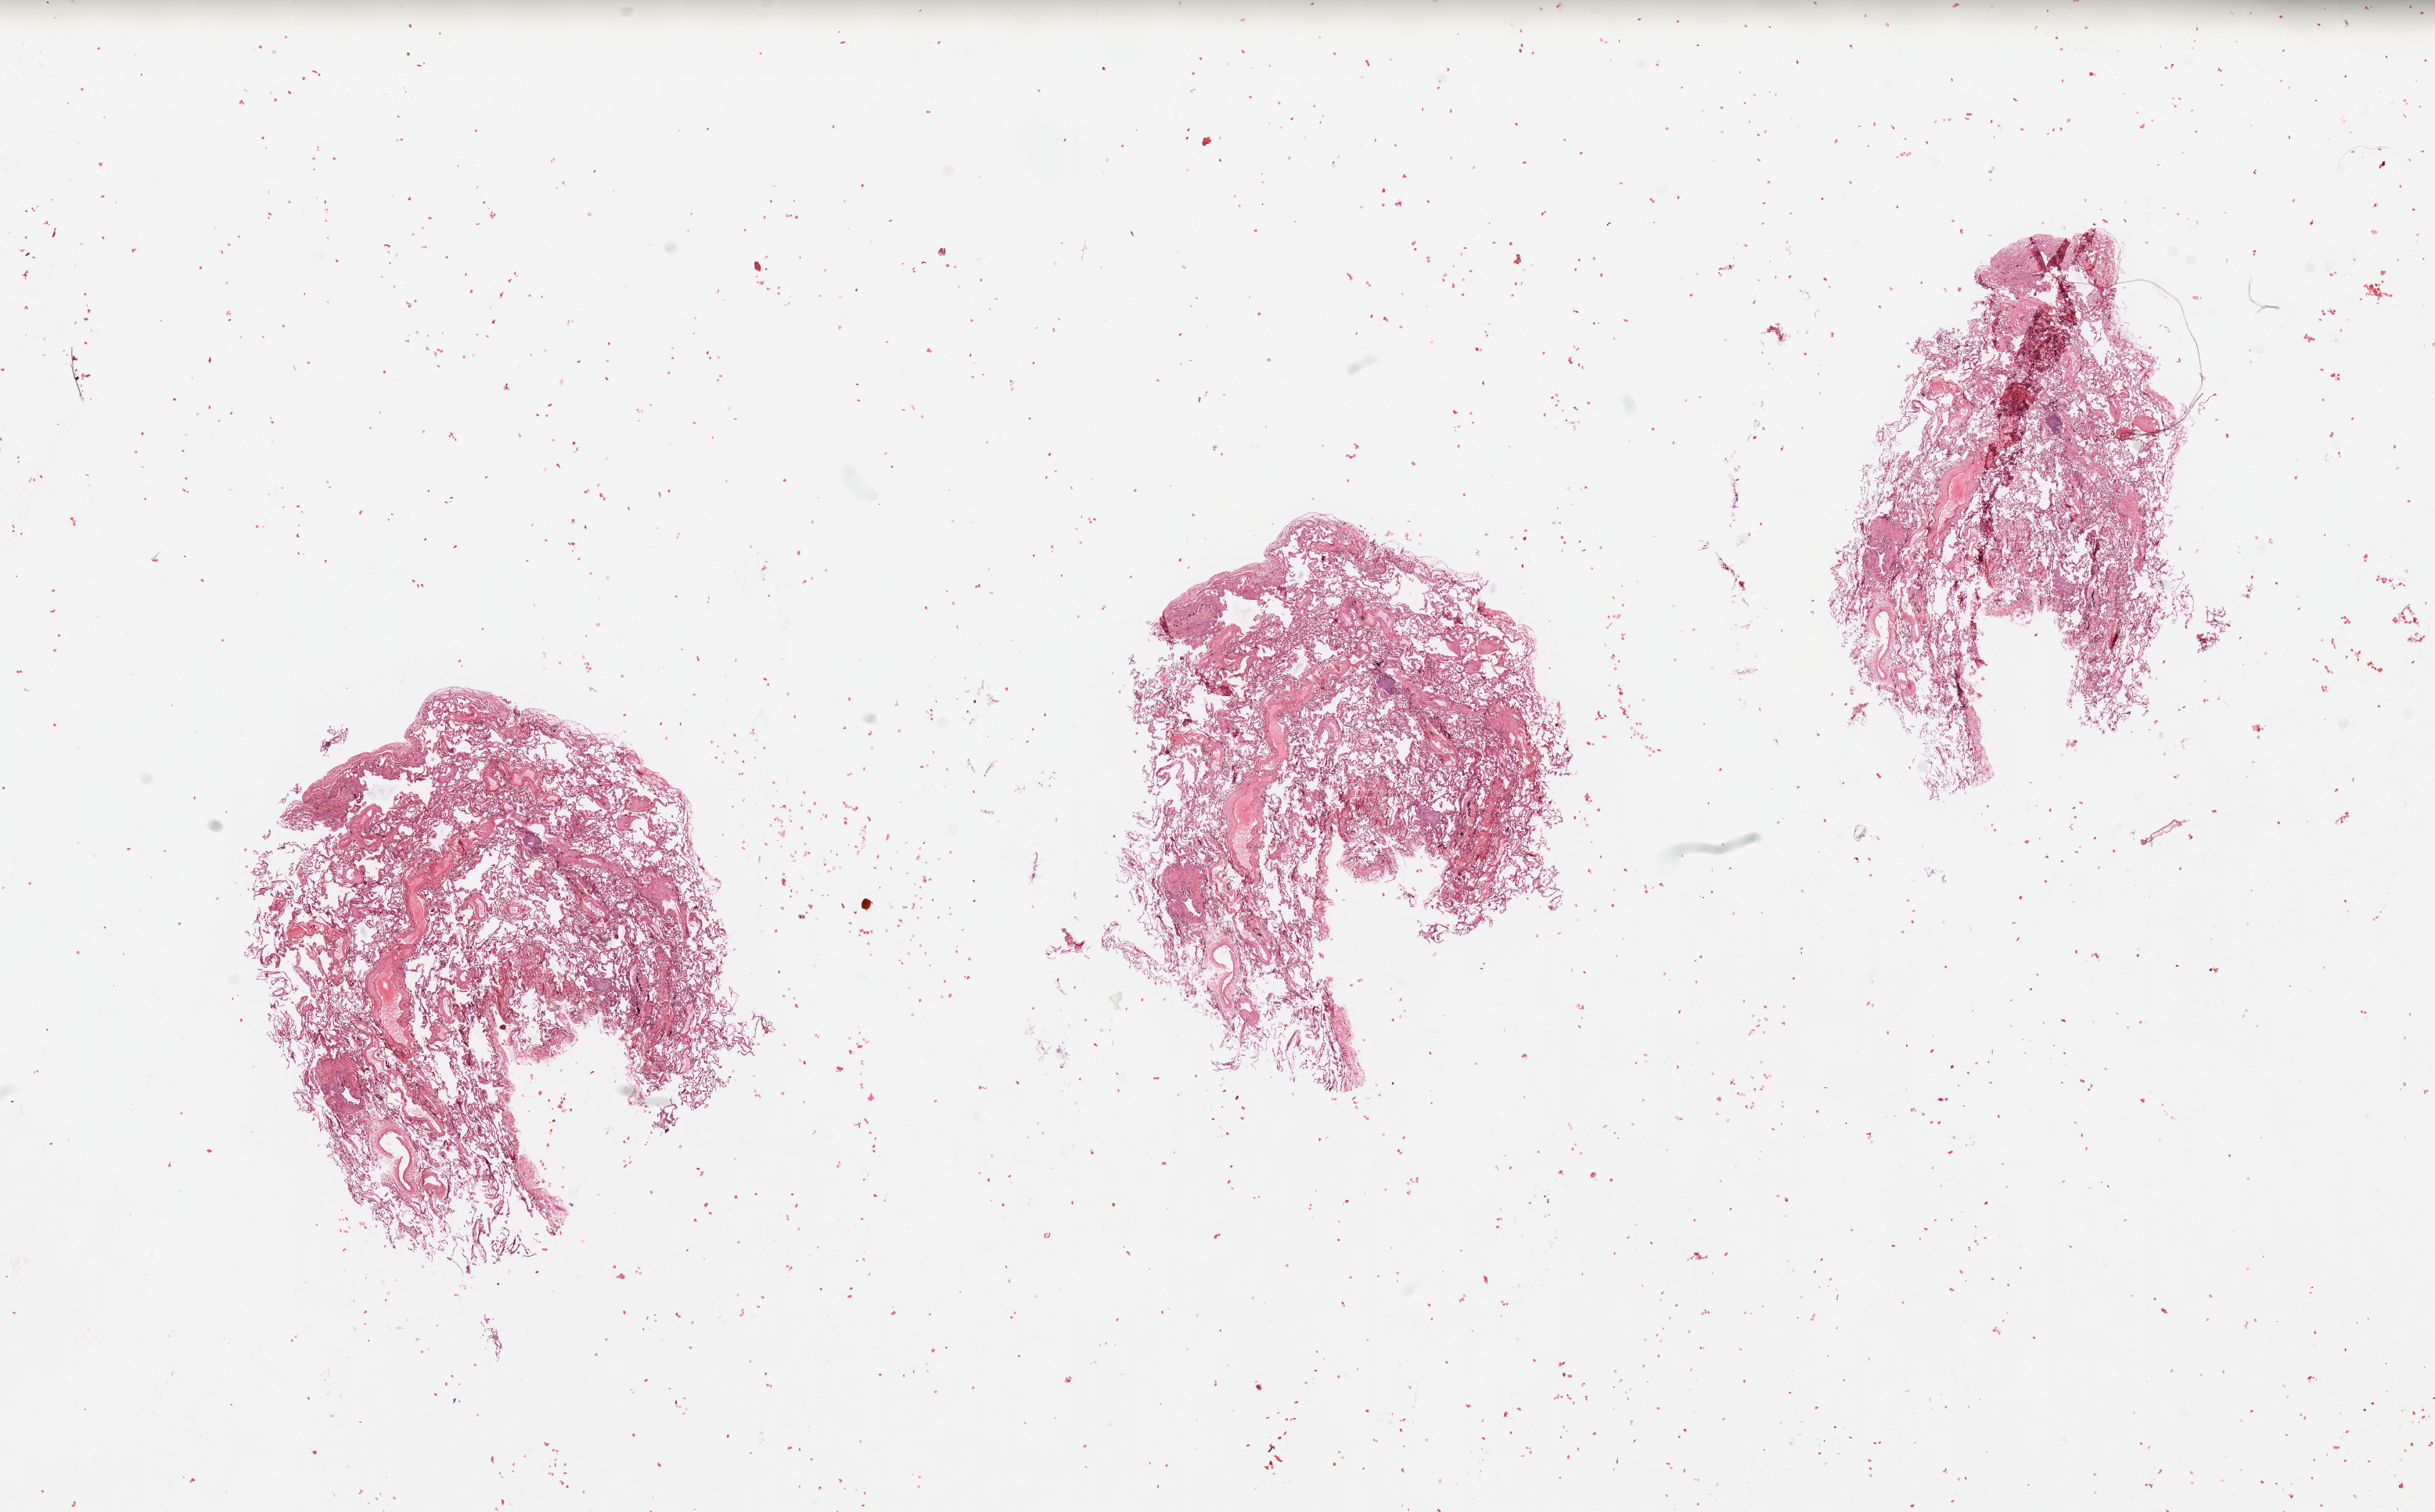
H&E-stained whole-slide image, whole scanned area (about 24.6 x 15.3 mm, slide scanned at 20x) shown as a low-resolution overview. Lung, normal (non-tumour) tissue. 69-year-old male patient.
• this section: normal (non-tumour) tissue from the same patient
• patient diagnosis: Squamous cell carcinoma, NOS